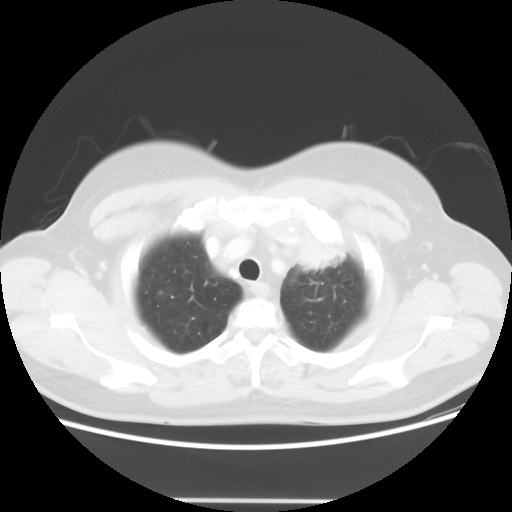
Chest CT, one axial slice; position 46 of 52 along the scan axis; reconstruction kernel STANDARD; lung window (W 1500 / L -600 HU); 5 mm slice thickness; 512 × 512 image matrix, field of view 382 × 382 mm. Female patient, age 52 years. From the clinical record (not read from this slice): clinical TNM (as recorded): T2 N3 M0.
Outlined on this slice (rectangle marked by the reading radiologist):
- lung tumour (recorded histology: adenocarcinoma): bounding box <288,225,351,274> (left, top, right, bottom; pixels)